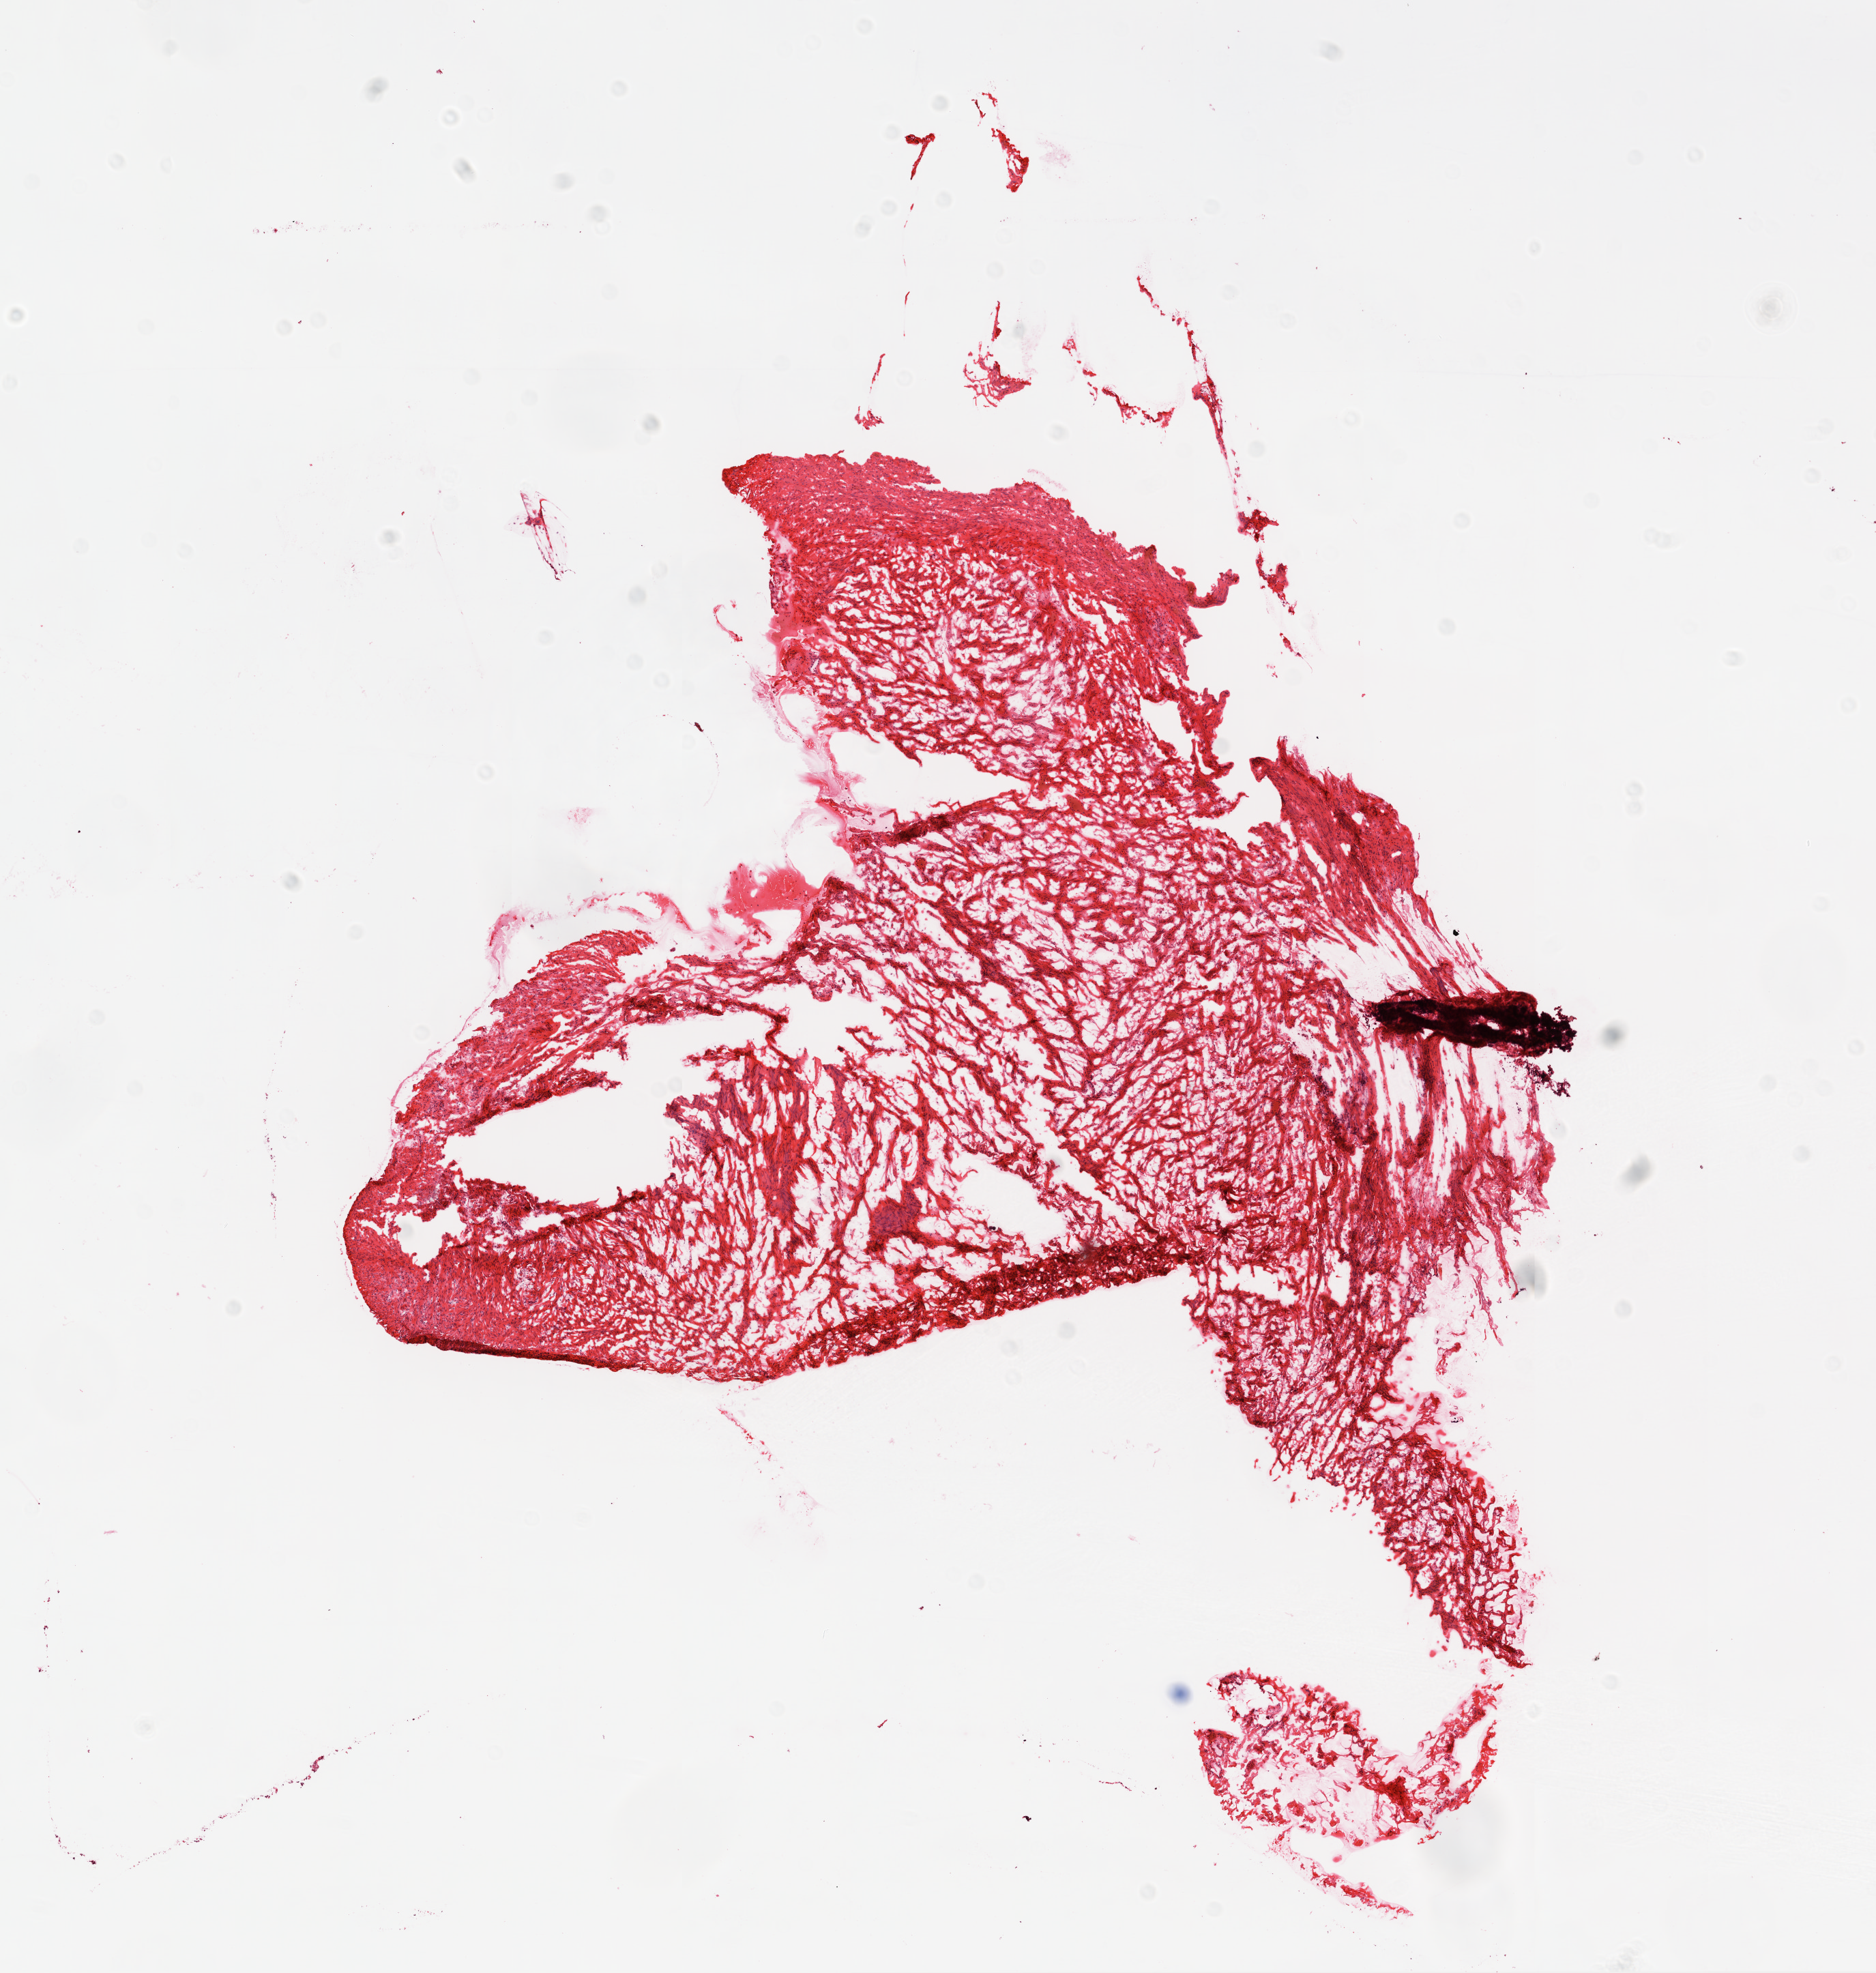
Digitized H&E-stained tissue section (whole slide), low-resolution overview of the scanned area, about 11.0 x 11.6 mm (from a 20x scan), frozen section from the top of the tissue portion, ovary, solid tissue normal (non-tumour tissue) sample. Patient: female, age at initial diagnosis 60 years.
This section: solid tissue normal sample (biorepository sample class). Patient diagnosis: Serous cystadenocarcinoma, NOS.